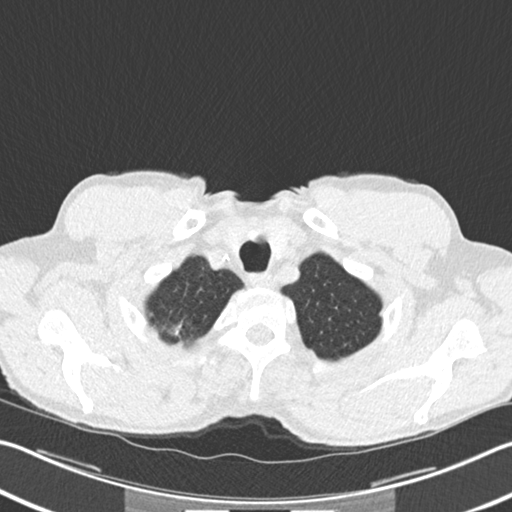
Chest CT (low-dose screening protocol), one axial image, second annual screen, lung window (W 1500 / L -600 HU), 2 mm slice thickness, 512 × 512 image matrix, field of view 342 × 342 mm. Male, age 62 years at enrolment. Former smoker at enrolment.
Expert reader's lesion annotation, bounding box <156,311,203,354> (left, top, right, bottom; pixels). The screening reader recorded 2 non-calcified nodules or masses ≥4 mm on this exam (right upper lobe, right upper lobe); which of them this box marks is not recorded. Official screen result: positive, change unspecified: nodule(s) >= 4 mm or enlarging nodule(s), mass(es), or other non-specific abnormalities suspicious for lung cancer. Lung cancer was diagnosed 5 days after this screen: bronchiolo-alveolar adenocarcinoma, NOS, right upper lobe, well differentiated (G1), stage IA (AJCC 6th edition), 15 mm at pathology.